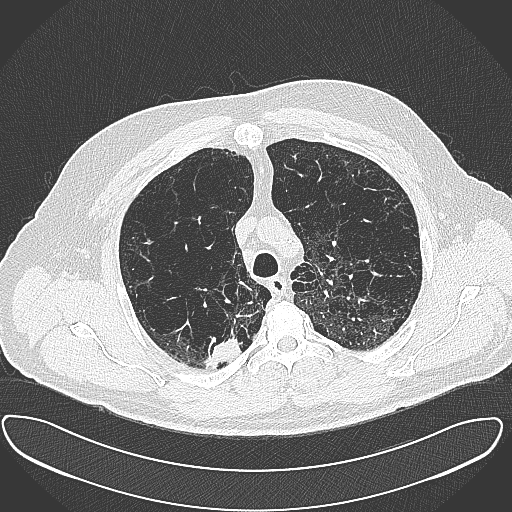
Axial slice from a low-dose chest CT screening exam, baseline annual screen, lung window (W 1500 / L -600 HU), 1 mm slice thickness, slice 87 of 385 in the series, 512 × 512 image matrix, field of view 408 × 408 mm. Male participant, aged 60 years at enrolment.
Lesion marked by an expert reader, box from (x=197, y=327) to (x=245, y=370) px. Reader record for this screening exam (exam-level; its link to the box is not recorded): non-calcified nodule or mass ≥4 mm, right upper lobe, 15 × 25 mm, spiculated (stellate) margins, soft tissue attenuation.